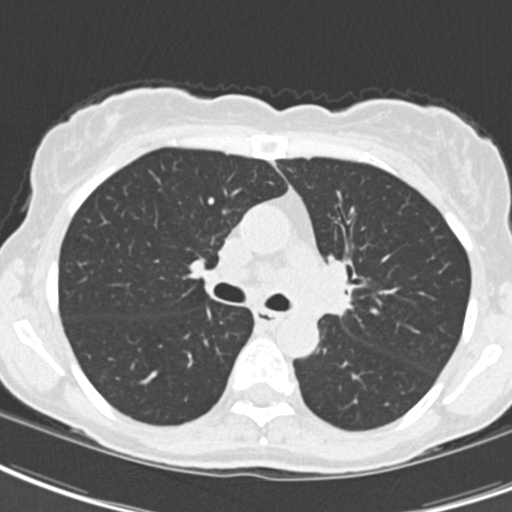
Low-dose screening chest CT, axial slice; baseline annual screen; lung window (W 1500 / L -600 HU); slice 64 of 189 in the series. Female participant, aged 62 years at enrolment.
Expert-annotated lung lesion, bounding box [x1, y1, x2, y2] px = [295, 248, 370, 332]. Screening reader's record for this exam (one nodule recorded; not confirmed to be the boxed lesion): non-calcified nodule or mass ≥4 mm, right upper lobe, 24 × 20 mm, smooth margins, ground glass attenuation. Note: the box lies in the patient's left hemithorax on this image, whereas the reader's record names the right lung; they may be different findings. Official screen result: positive, change unspecified: nodule(s) >= 4 mm or enlarging nodule(s), mass(es), or other non-specific abnormalities suspicious for lung cancer. Later outcome: lung cancer diagnosed 24 days after this screen — oat cell carcinoma, left hilum, left main stem bronchus, stage IIIB (AJCC 6th edition), 50 mm at pathology.